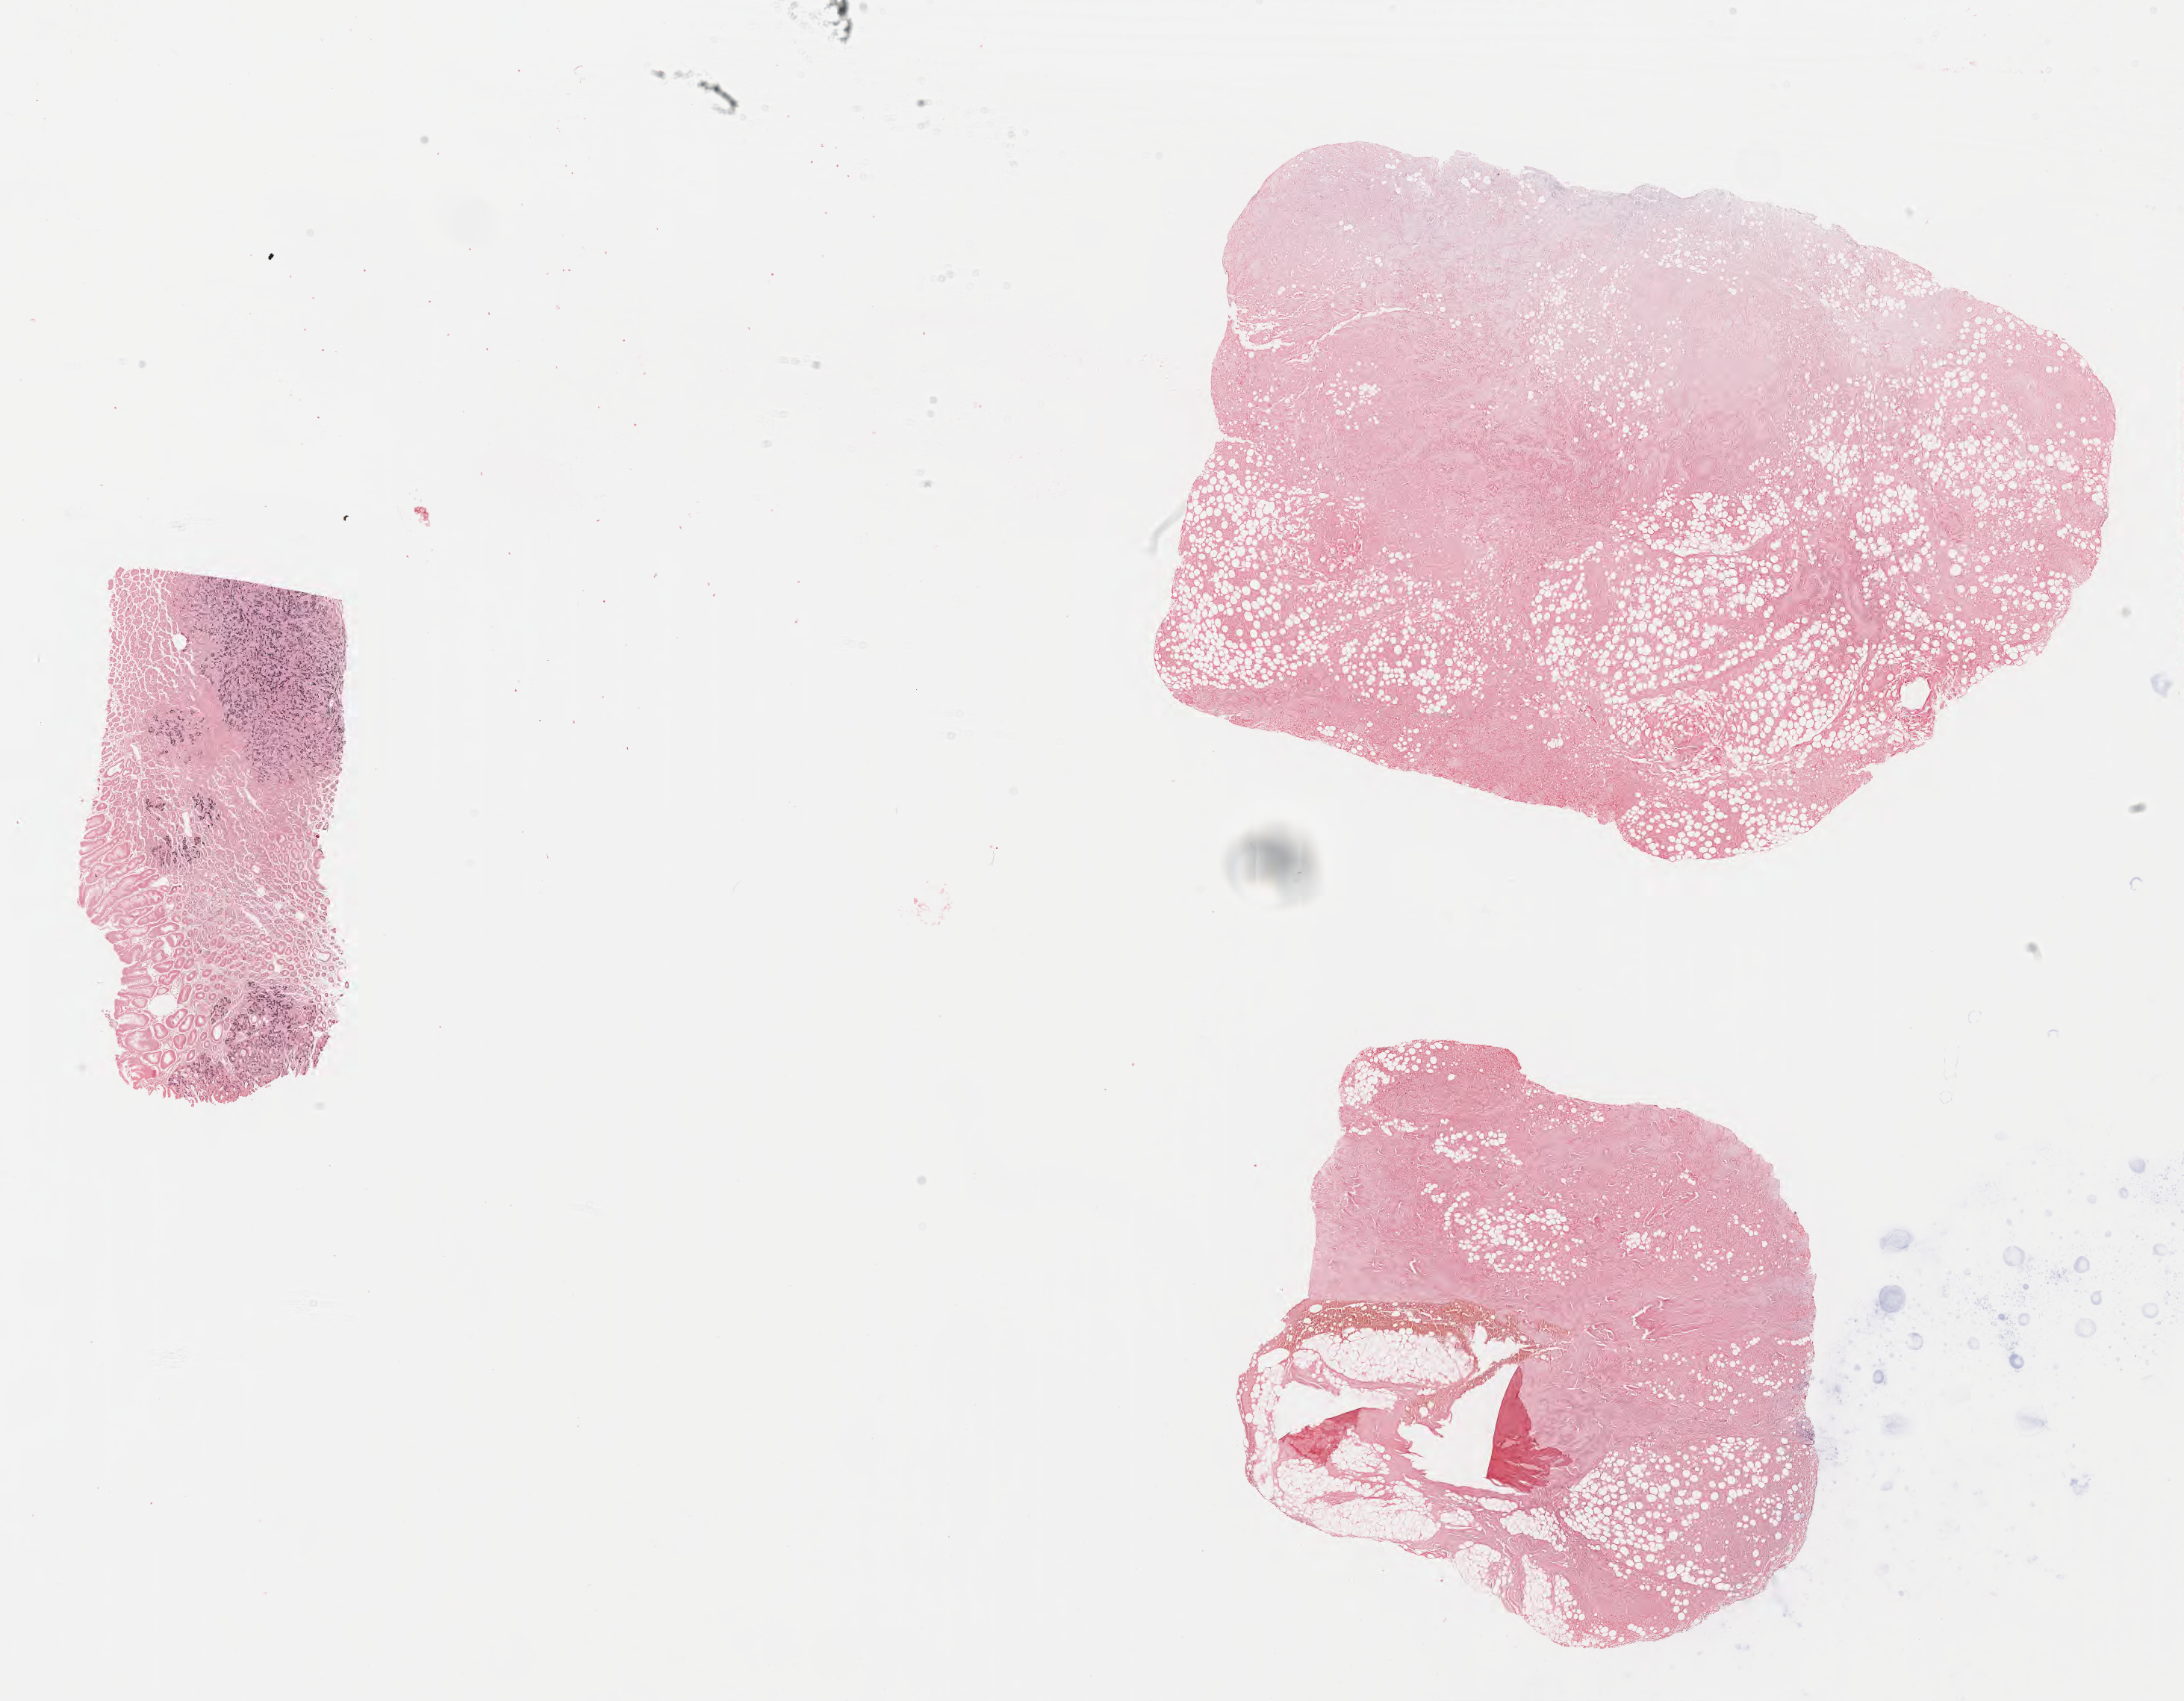
In-situ hybridisation whole-slide image, Epstein–Barr virus-encoded RNA (EBER) probe — low-resolution overview of the scanned area, about 23.6 x 18.4 mm; tumor tissue; anatomic site: kidney. Patient male; age 63 years.
Diagnosis: Diffuse large B-cell lymphoma, NOS.